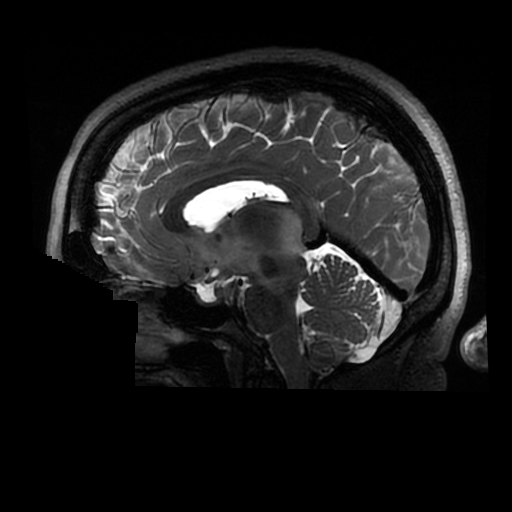
Brain MRI from a brain-tumour surgery series, one sagittal slice. Position 157 of 320 along the scan axis. 0.6 mm slice thickness. 512 × 512 image matrix, field of view 240 × 240 mm. Case-level facts recorded for this patient, not image findings: histopathology: Astrocytoma; WHO grade: 2; IDH mutation: yes.
Structures marked on this image (expert manual segmentation):
- tumour: bounding box (x1, y1, x2, y2) in pixels: (277, 208, 304, 259)